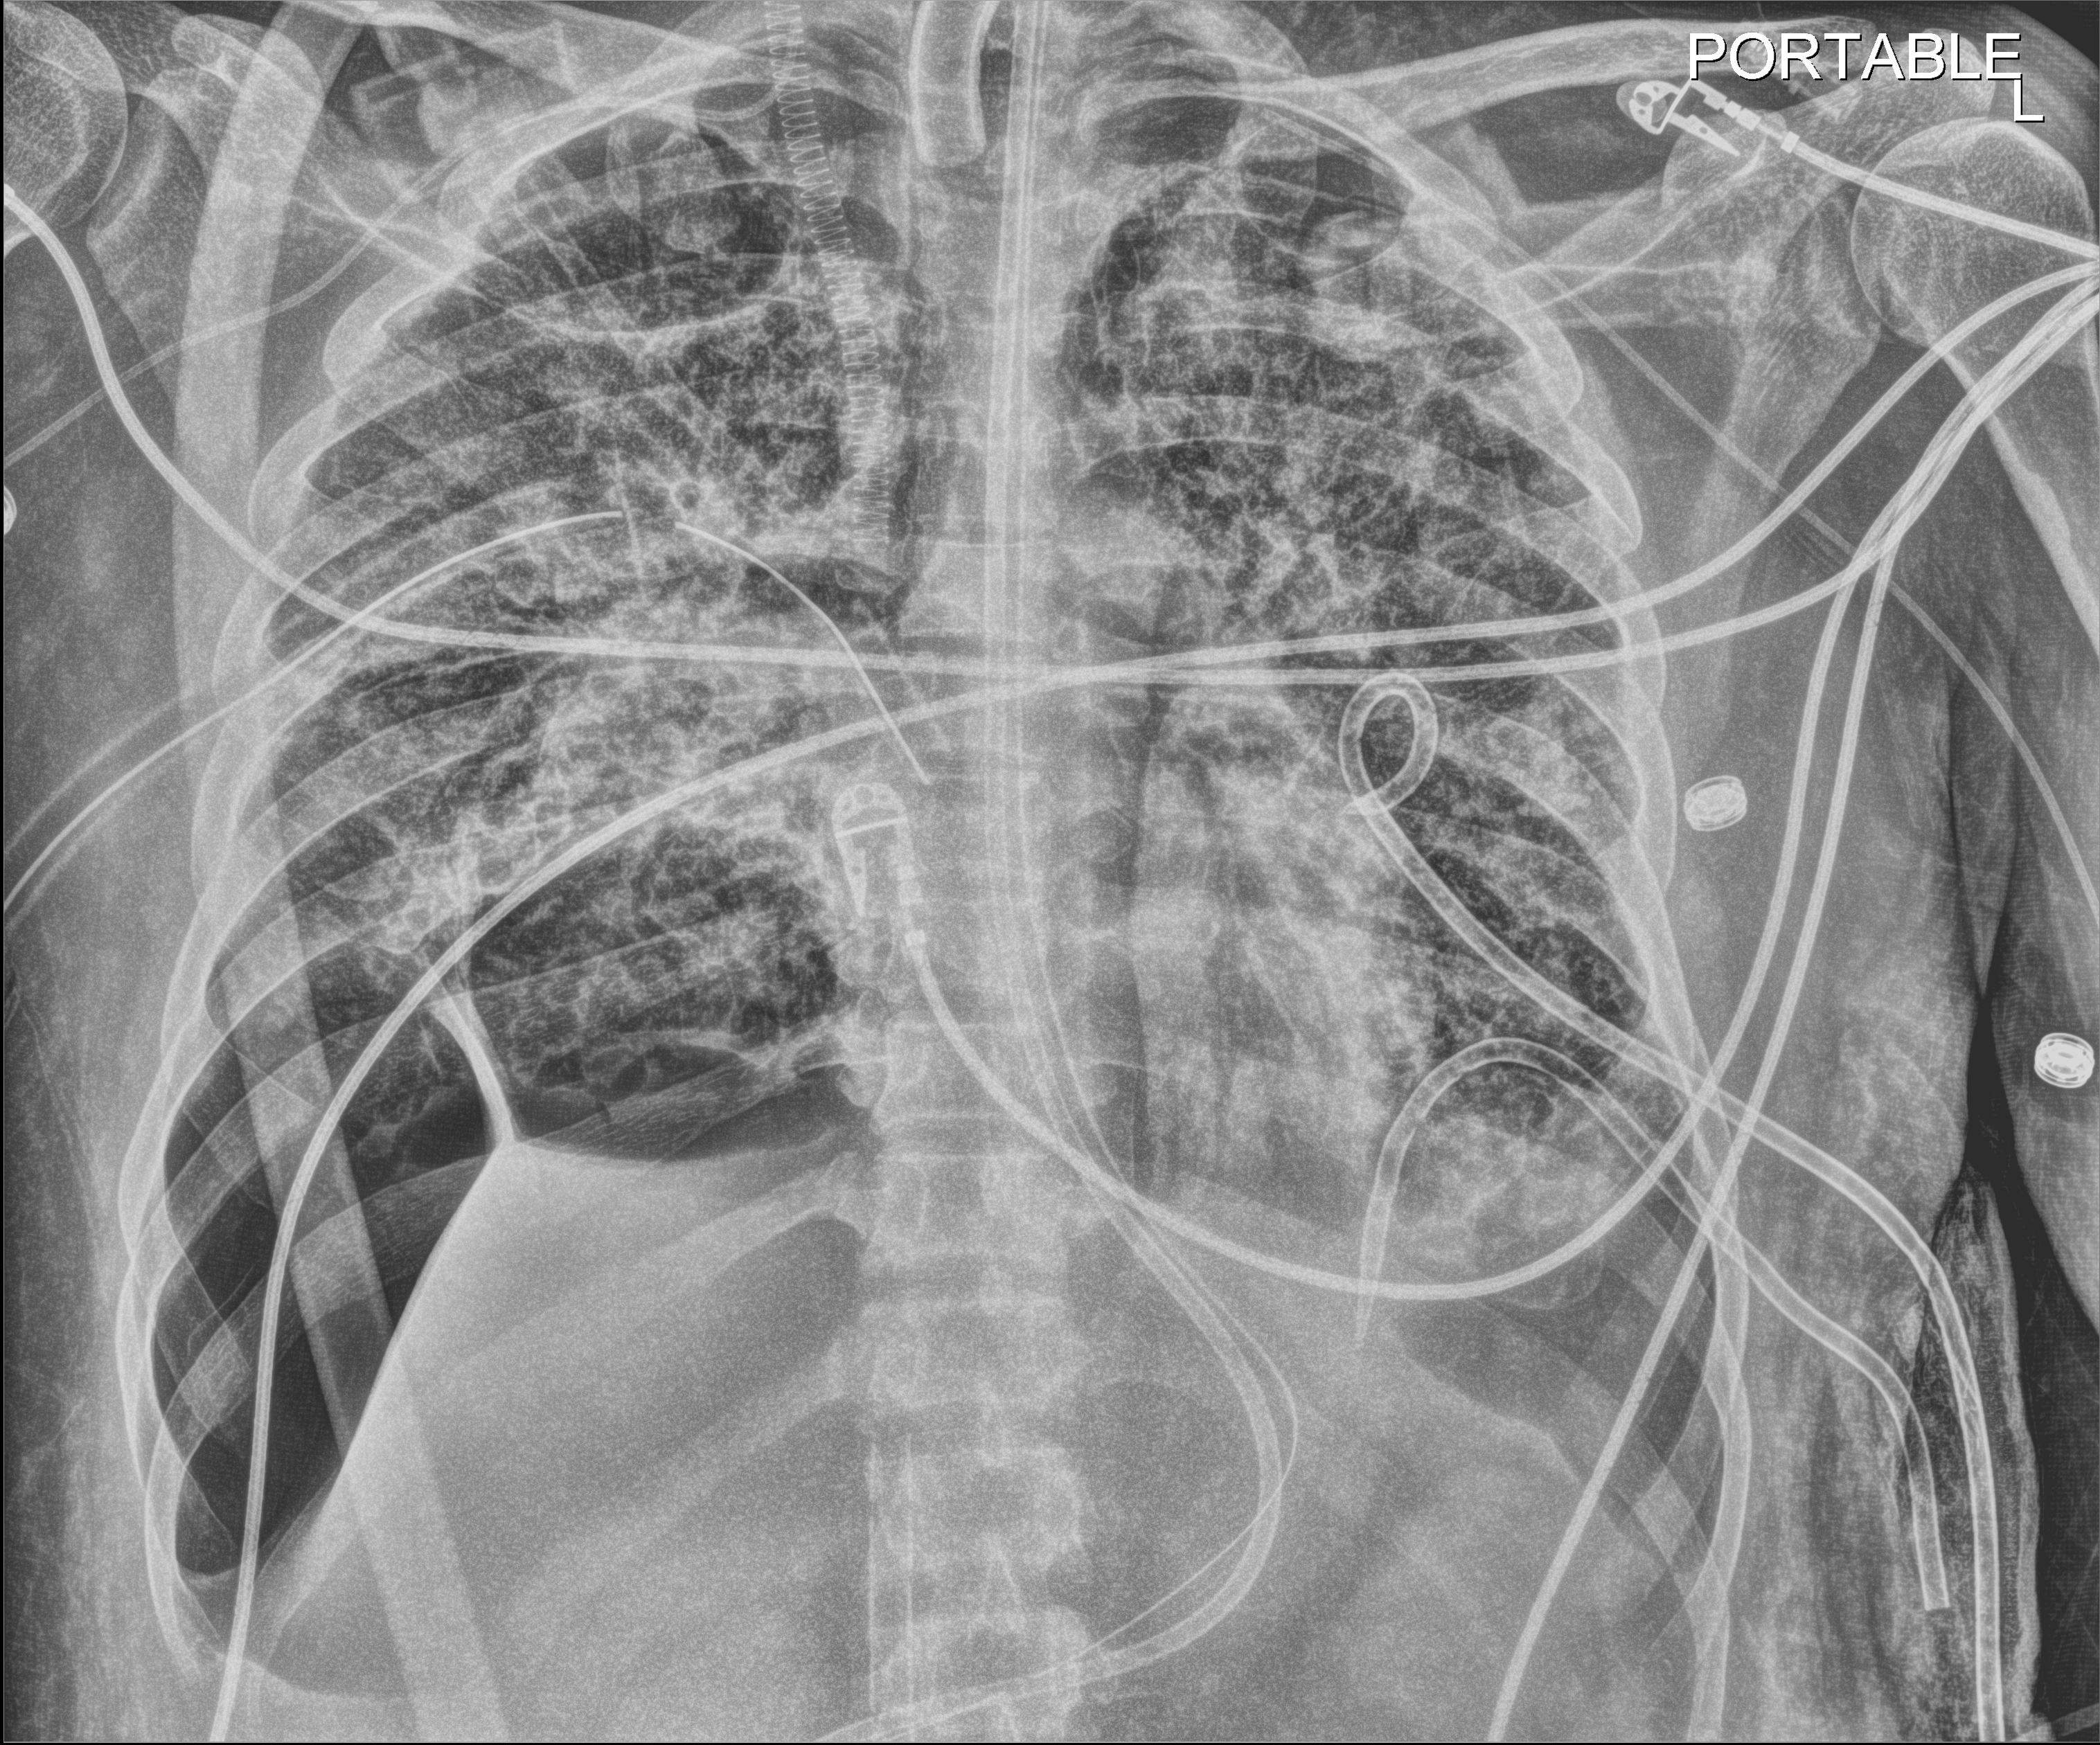
Bedside chest radiograph (digital radiography); anteroposterior (AP) projection. Patient hospitalised with COVID-19, aged 18–59 years.
Admission-level facts for this patient (not findings on this image; timing relative to this image not recorded): admitted to intensive care during this hospital stay: yes; COPD (admission record): no.